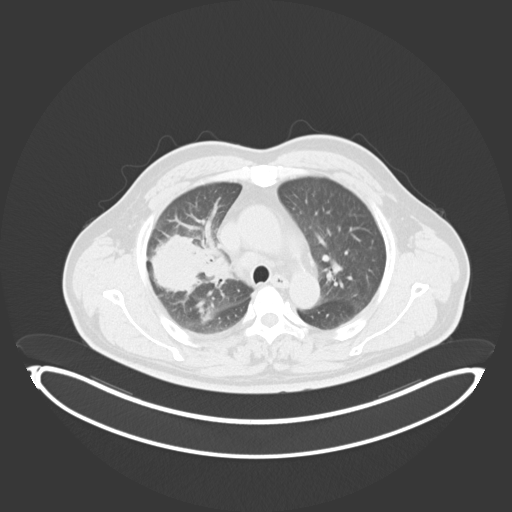
Chest CT, one axial slice. Slice 220 of 284 in the series (ordered by position). Reconstruction kernel B30f. 120 kVp. Lung window (W 1500 / L -600 HU). 3 mm slice thickness. 512 × 512 image matrix. Patient: male, 55 years. From the clinical record (not read from this slice): clinical TNM (as recorded): T3 N2 M1.
Structures marked on this image (bounding box drawn by a radiologist):
- lung tumour (recorded histology: adenocarcinoma): bounding box (x1, y1, x2, y2) in pixels: (146, 233, 216, 295)